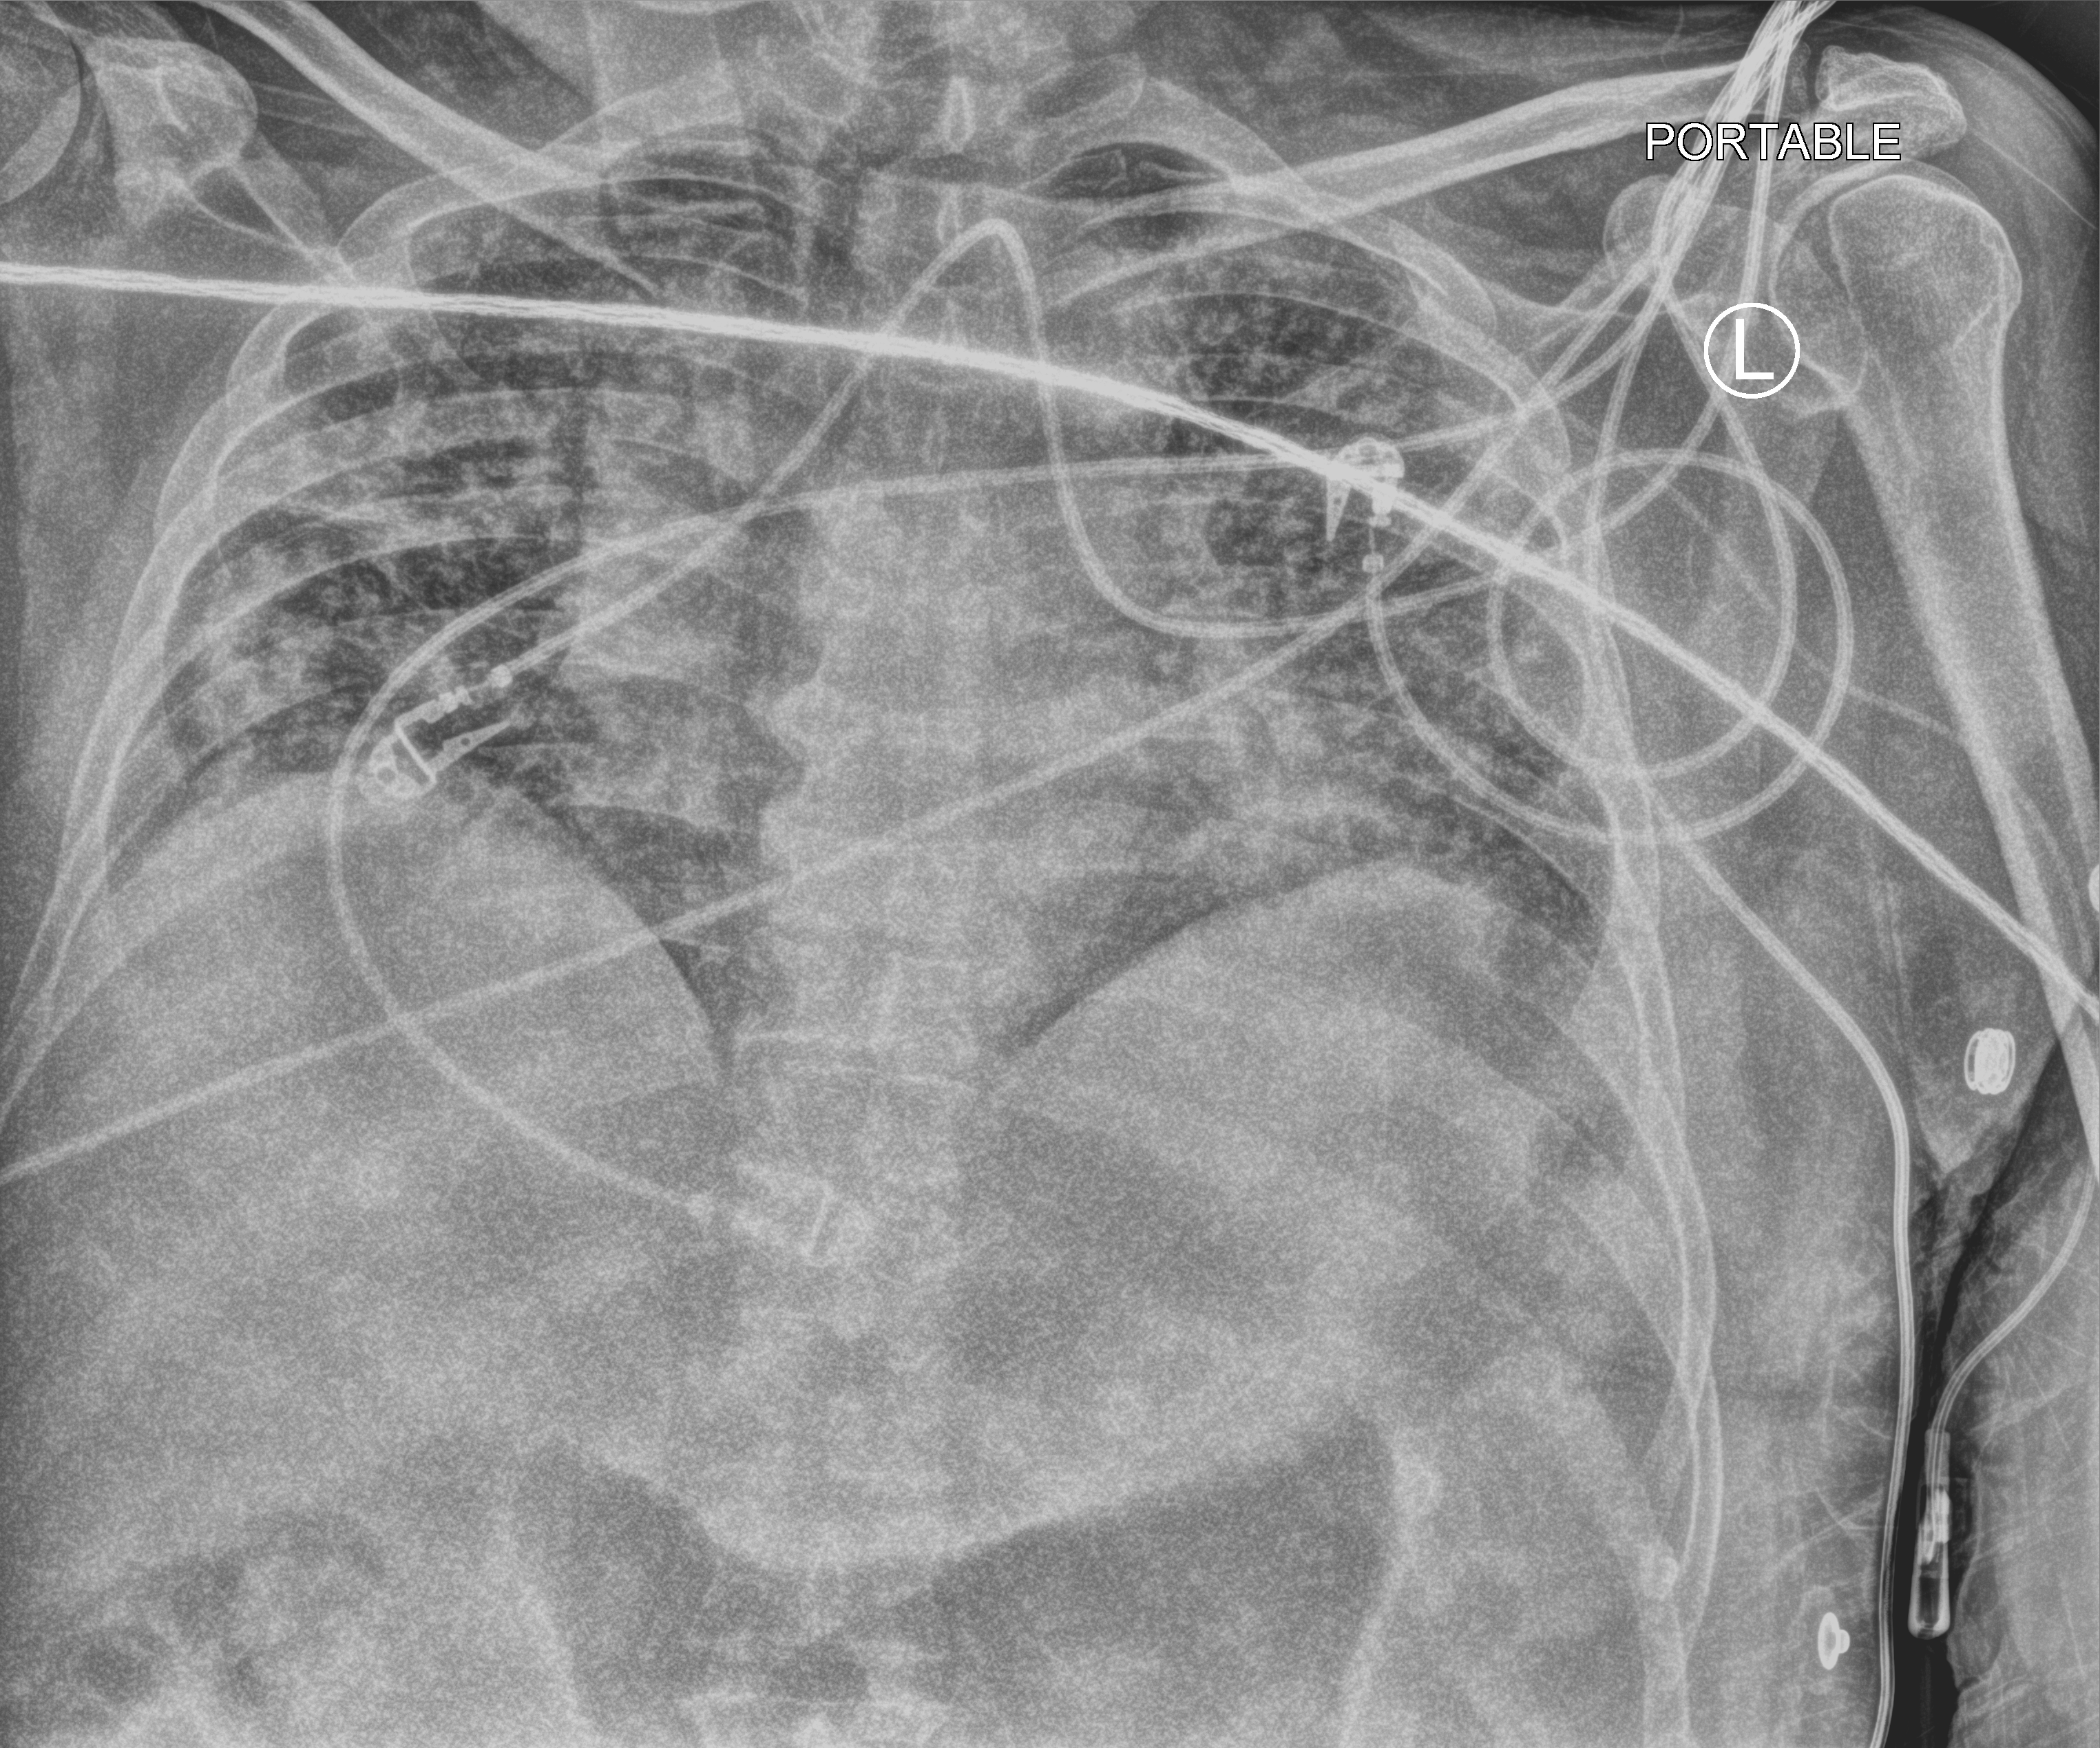
Portable chest radiograph, anteroposterior (AP) projection. Male patient hospitalised with COVID-19, age 60–74 years.
From the hospital-stay record, not from the radiograph (when in the stay this image was taken is not recorded):
- hypertension (admission record): yes
- admitted to intensive care during this hospital stay: yes